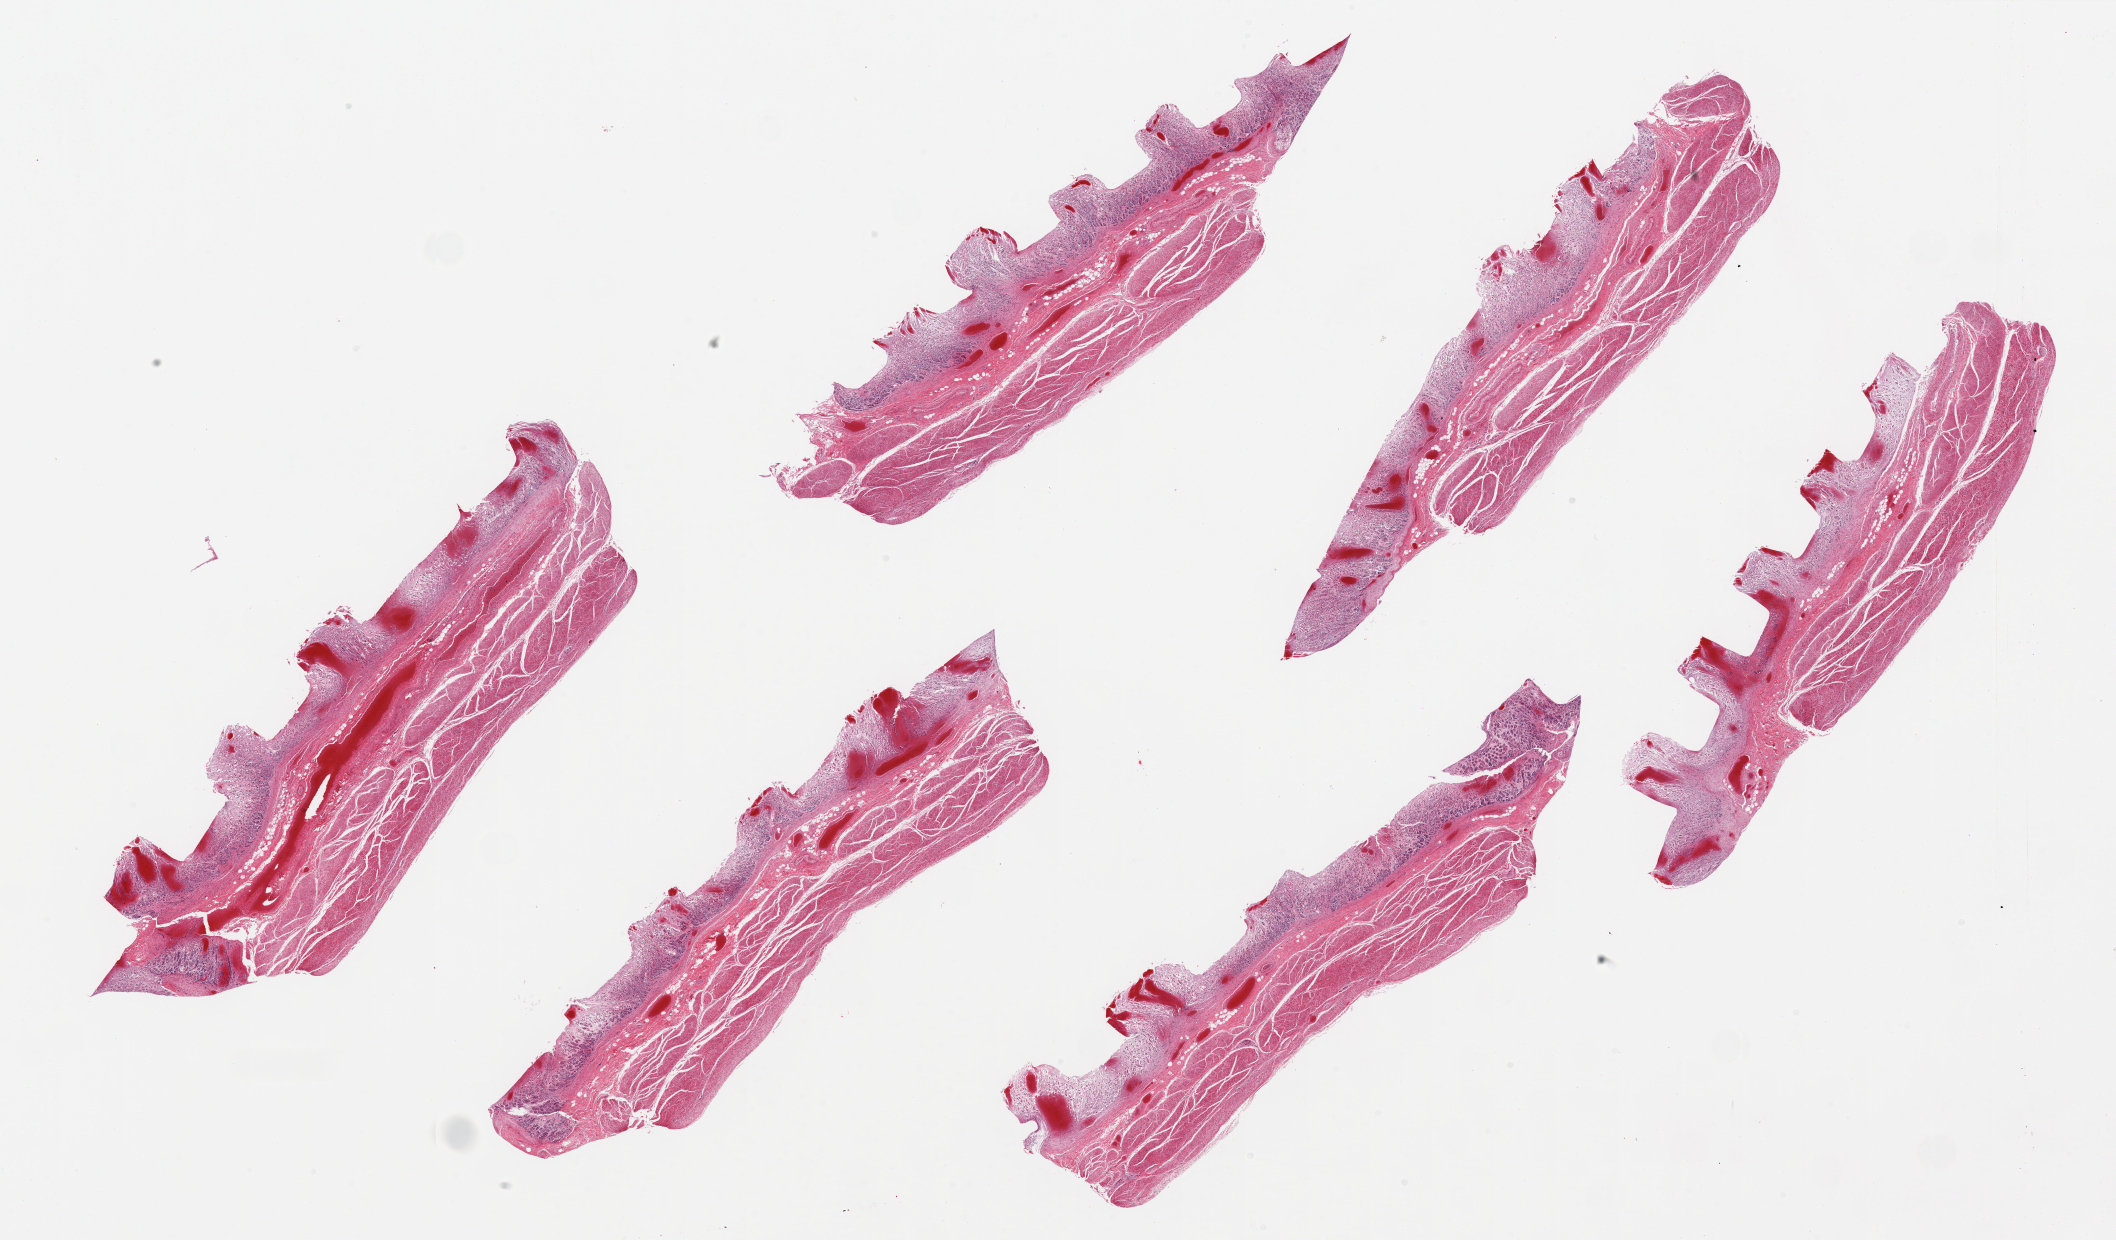
Hematoxylin and eosin (H&E) whole-slide image, brightfield, a low-resolution overview of the entire scanned area, about 33.5 x 19.6 mm; PAXgene-fixed, paraffin-embedded tissue; sampled site (target tissue): stomach; donor tissue sample. Donor: male.
• review note (as recorded): 6 pieces up to 11x3 mm; hemorrhagic and necrotic/autolyzed mucosa; muscle slightly autolyzed